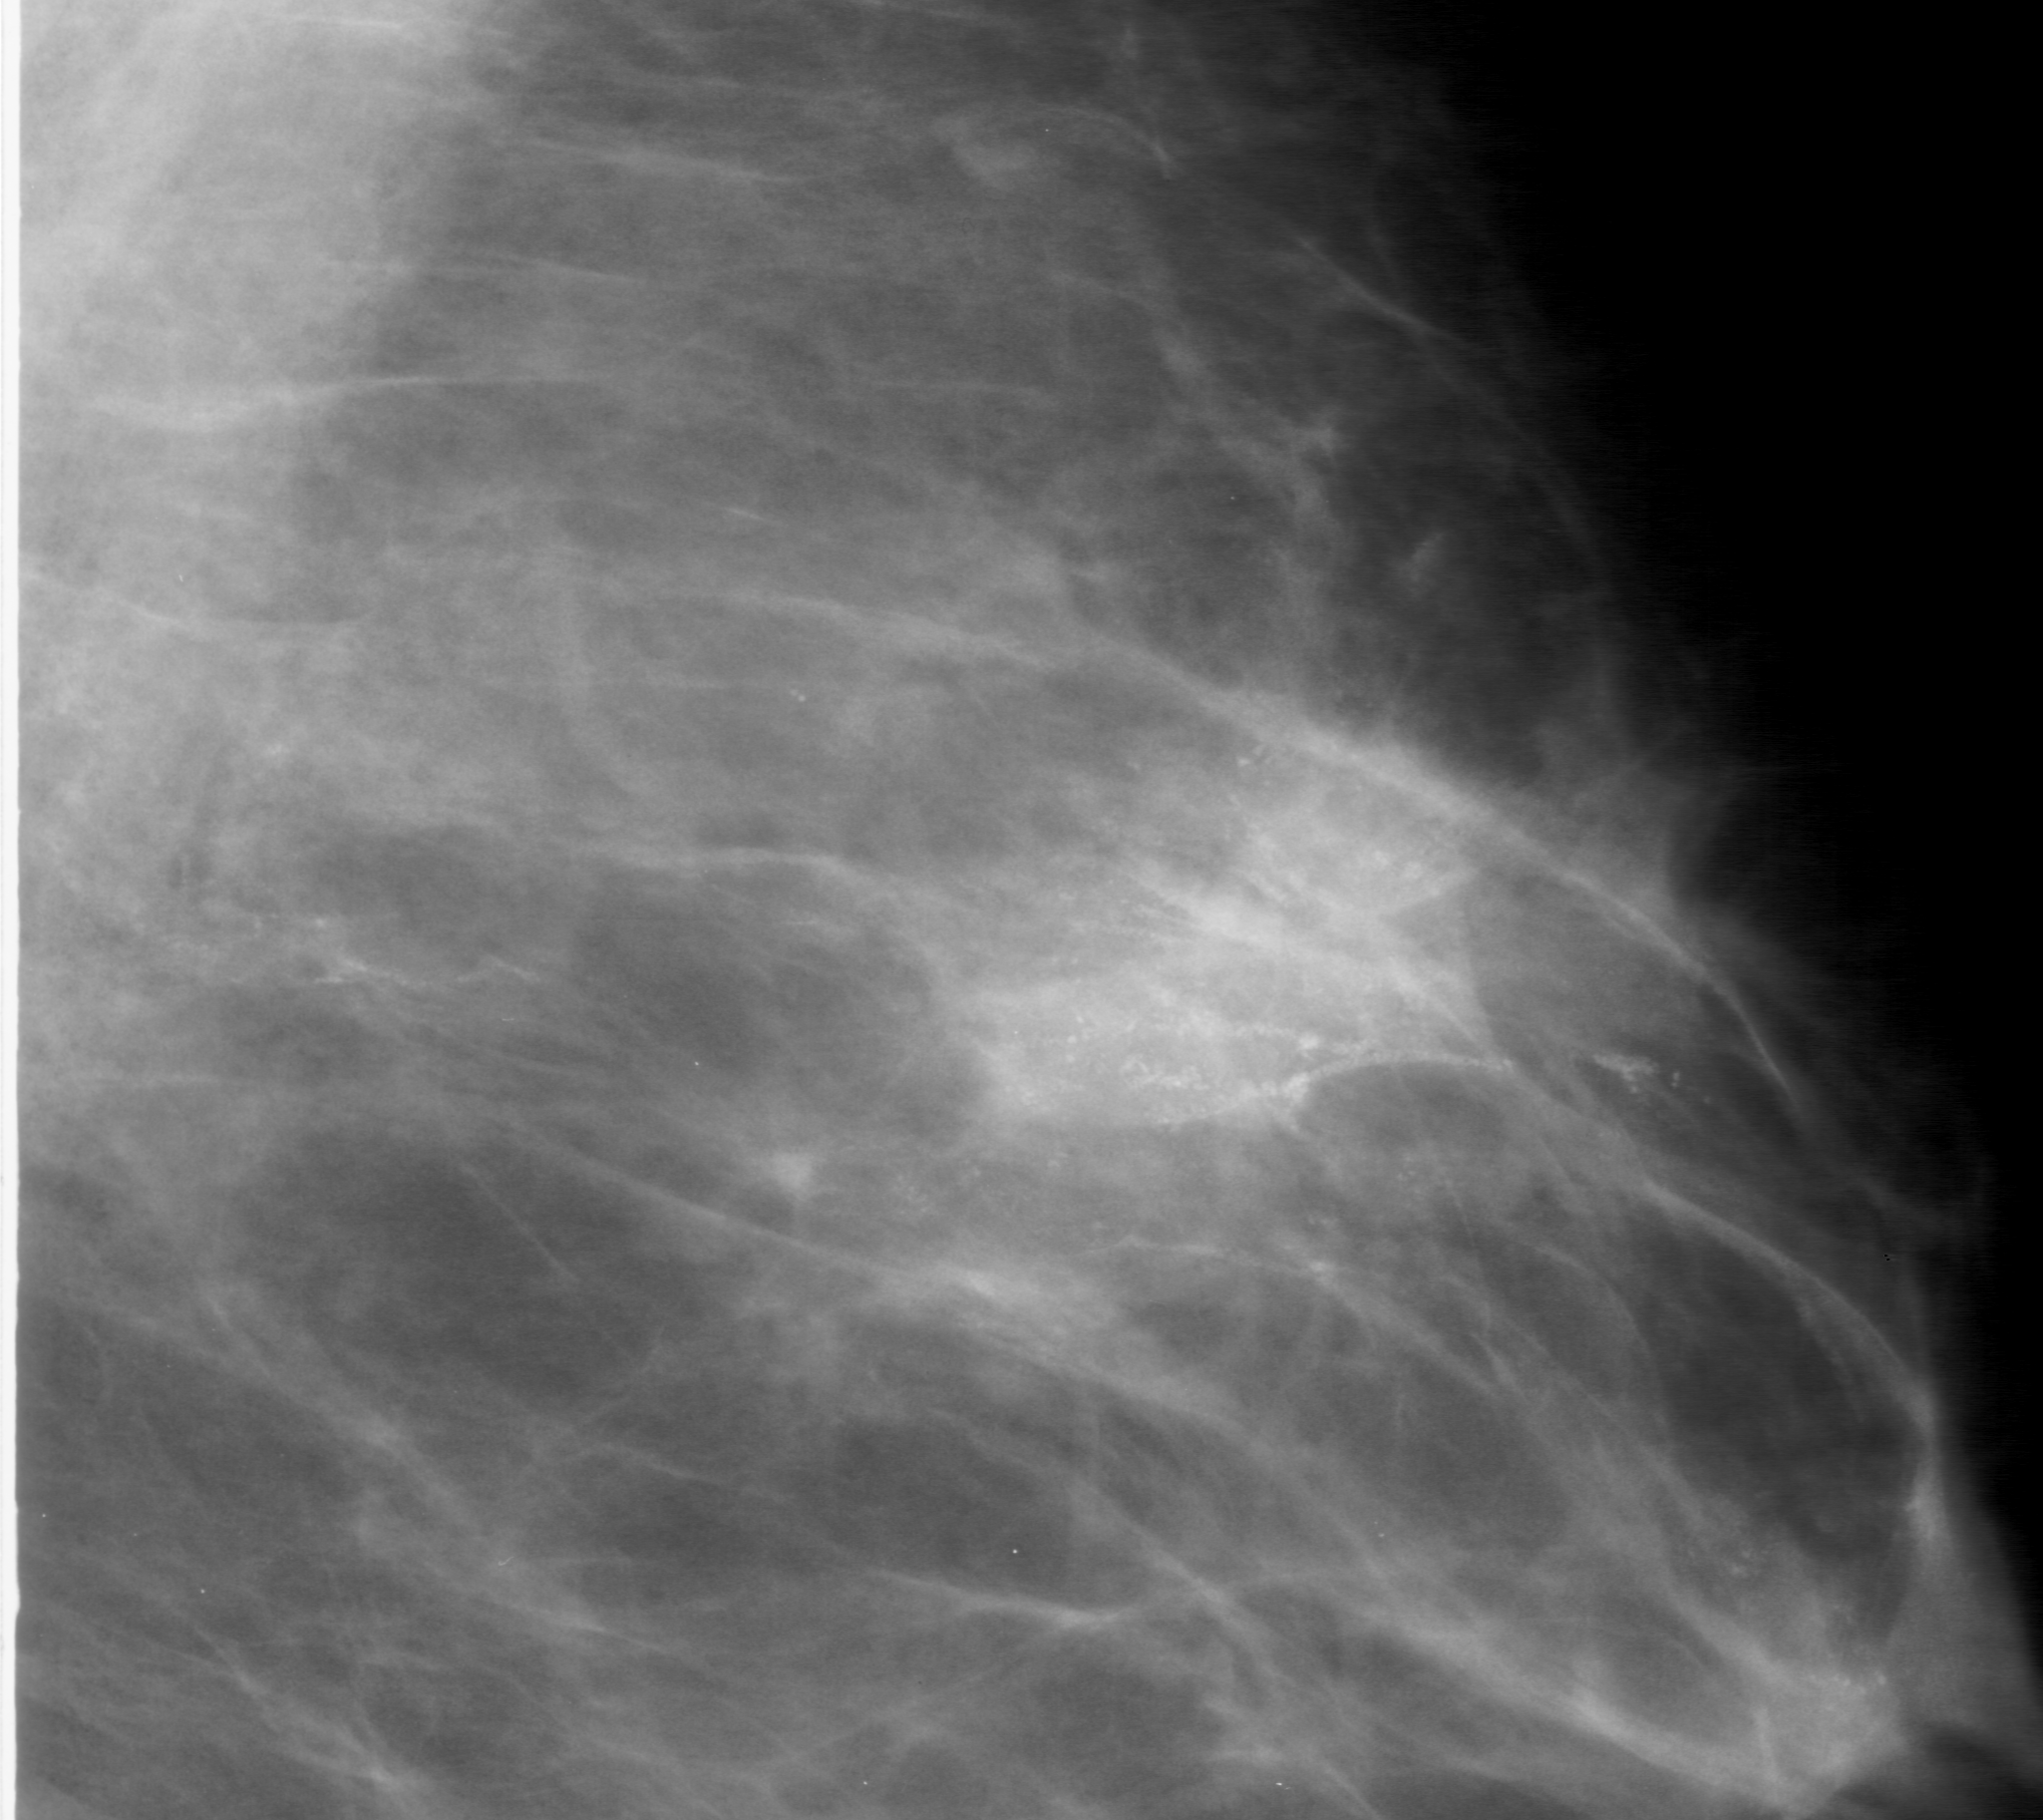
Region of interest cut from a scanned film mammogram (one marked finding), left breast, MLO view.
Marked abnormality: calcifications, morphology amorphous, distribution linear; BI-RADS assessment category 5; pathology (as recorded): malignant.